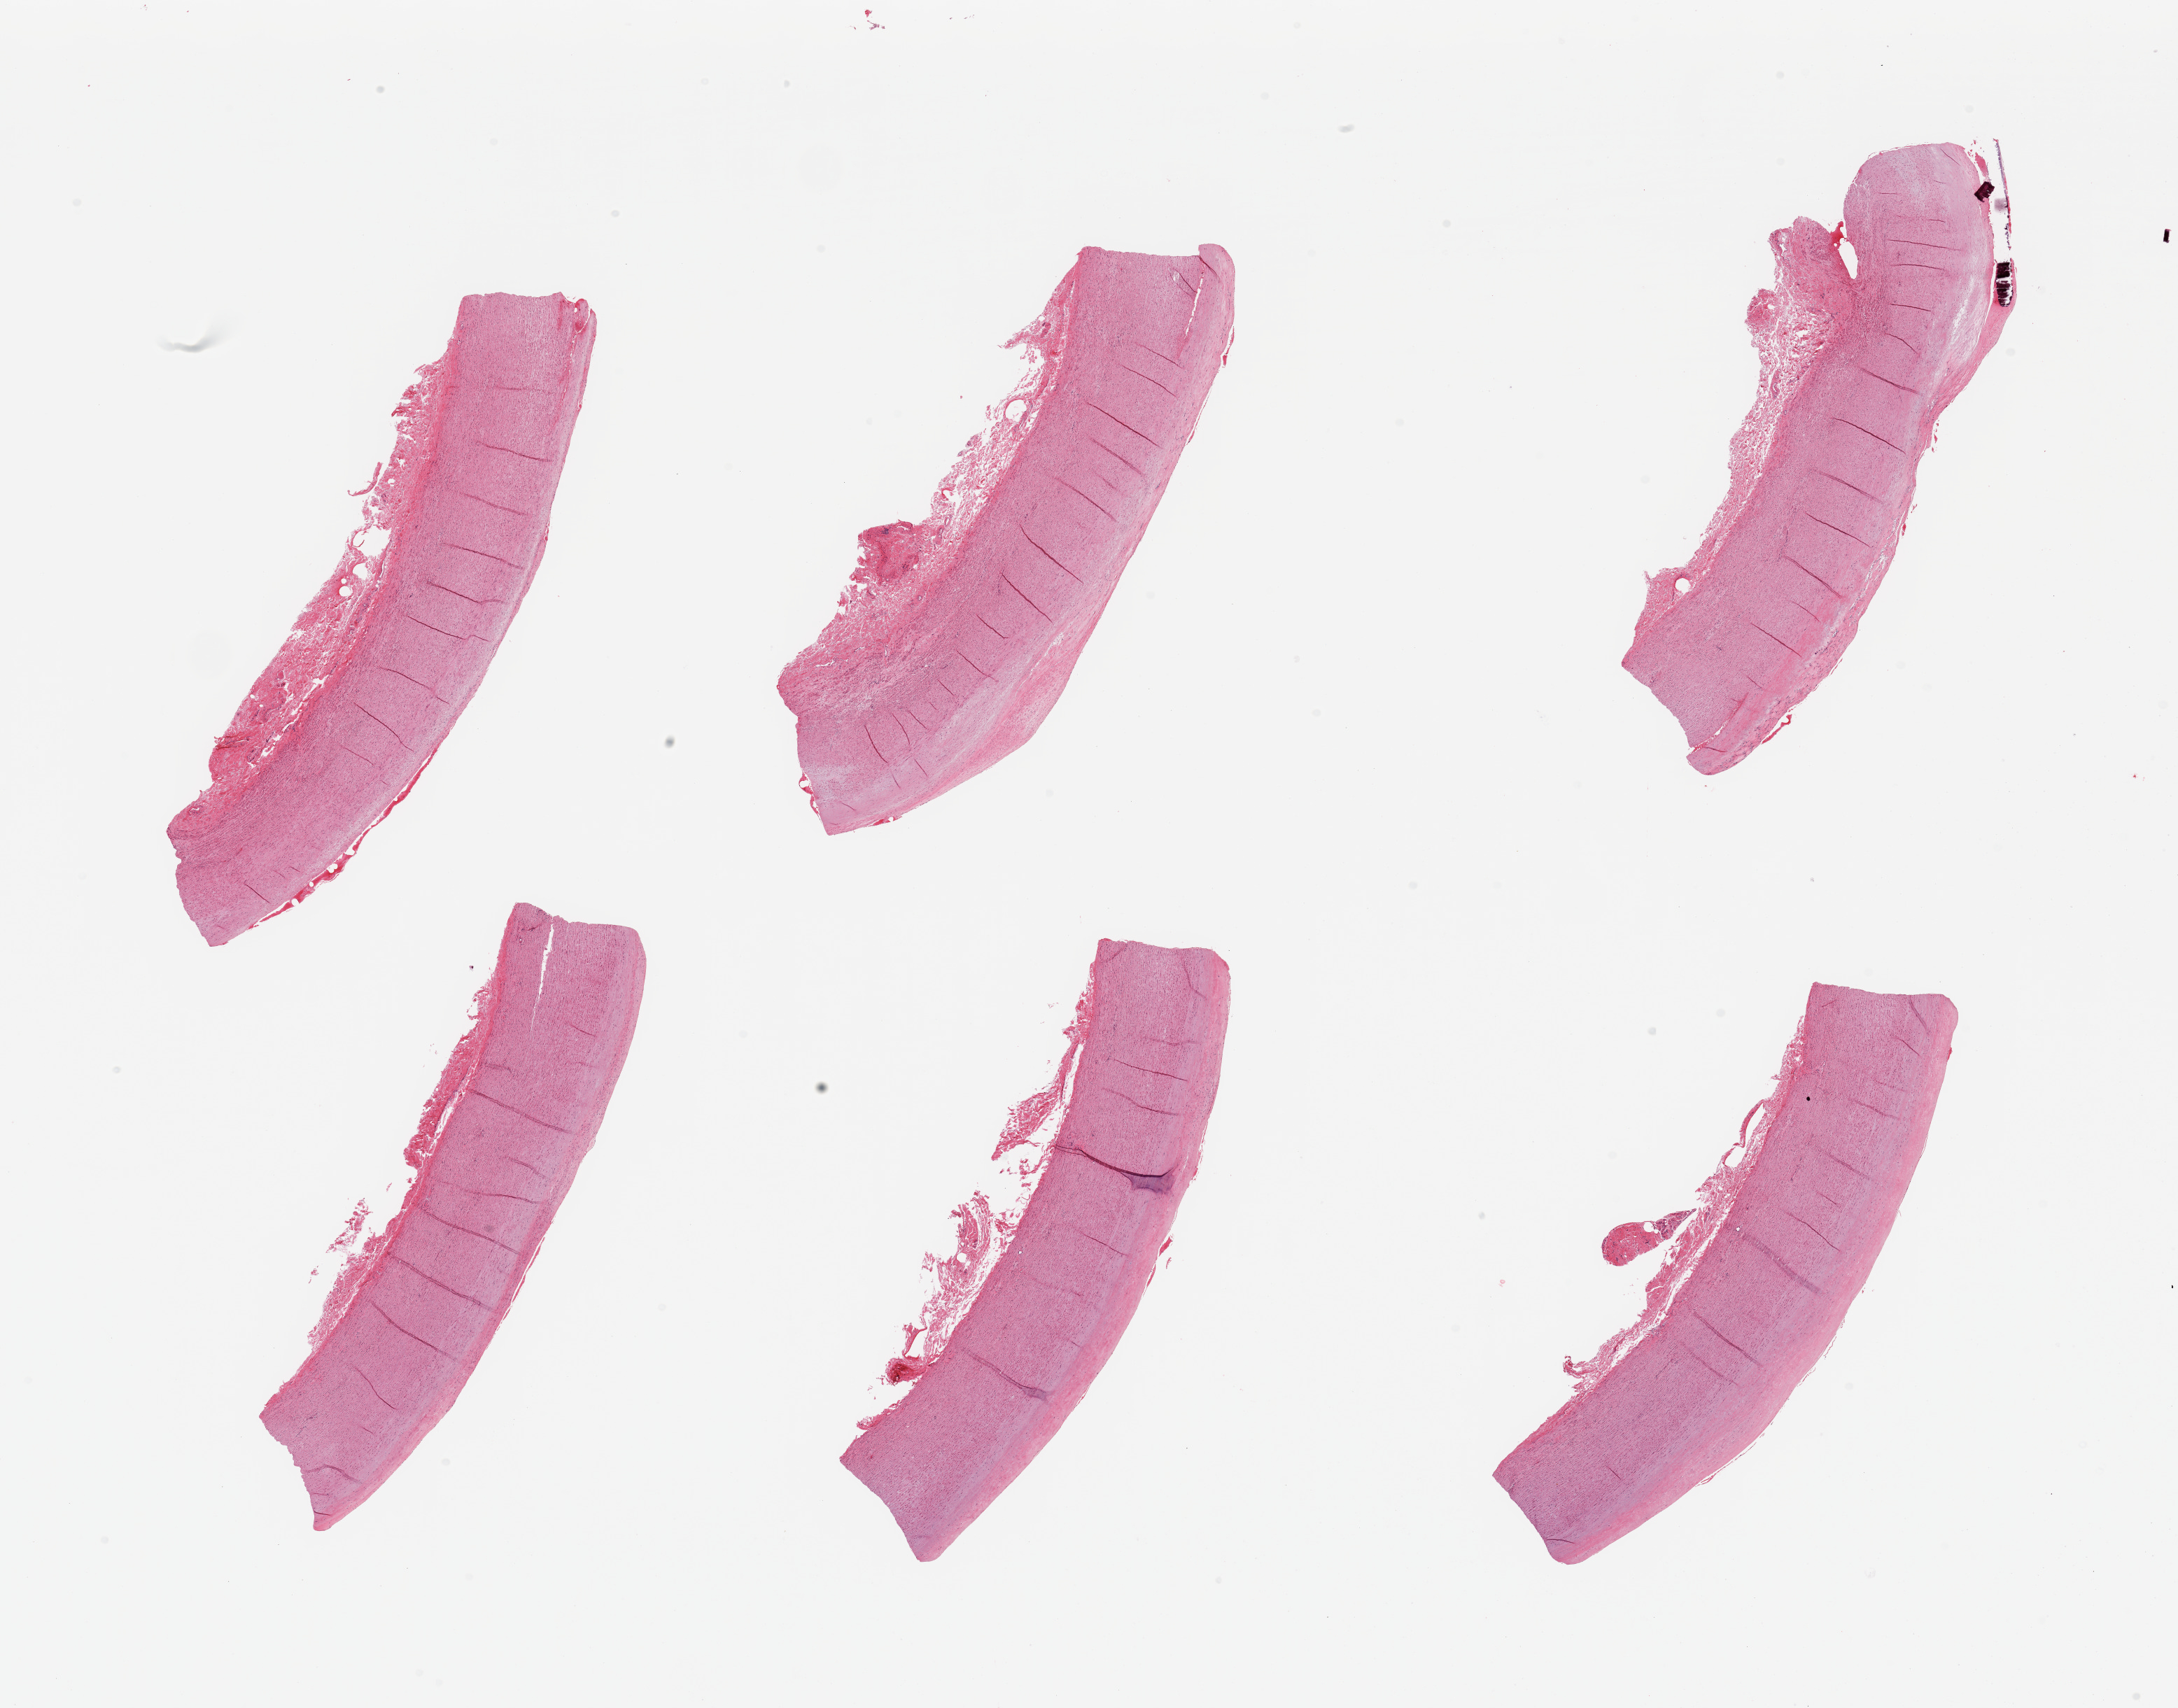
Haematoxylin and eosin whole-slide image, shown as a low-resolution overview of the whole scanned area (about 24.6 x 19.3 mm, acquisition: 20x scan). PAXgene-fixed paraffin-embedded (PFPE) section. Section of aorta (target tissue). Donor tissue sample.
• pathologist's review note for this sample: 6 pieces; atherosclerosis, focal calcification